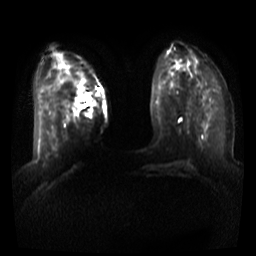
Breast MRI, one axial slice; diffusion-weighted series; image 2 of 4 stored at this slice position (different b-values; order by instance number); 3 T; 256 × 256 image matrix. Female patient.
Outlined on this slice (outlined manually by an expert reader):
- tumour on diffusion-weighted imaging: bounding box (x1, y1, x2, y2) in pixels: (77, 103, 88, 107)